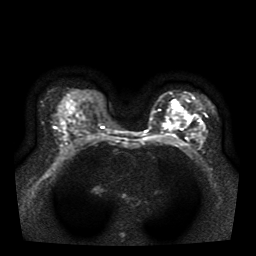
Breast MRI, one axial slice. Position 24 of 39 along the scan axis. Diffusion-weighted series; image 2 of 4 stored at this slice position (different b-values; order by instance number). 1.5 T. 5 mm slice thickness. 256 × 256 image matrix, field of view 330 × 330 mm. Female patient.
Structures marked on this image (outlined manually by an expert reader):
- tumour on diffusion-weighted imaging: bounding box (x1, y1, x2, y2) in pixels: (163, 111, 192, 129)